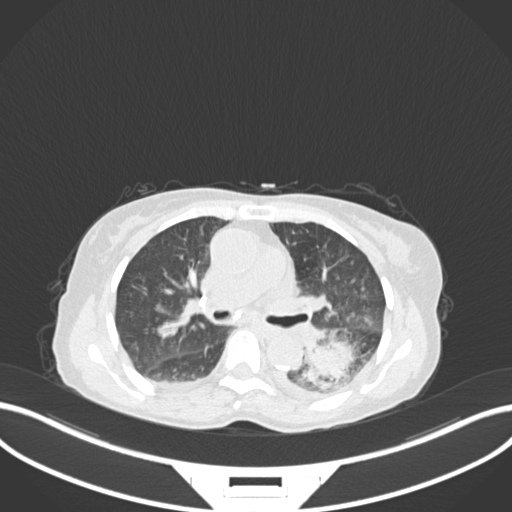
Chest CT, one axial slice; slice 103 of 233 in the series (ordered by position); reconstruction kernel B30f; lung window (W 1500 / L -600 HU); 1 mm slice thickness; 512 × 512 image matrix, field of view 400 × 400 mm. Patient: female, 78 years. From the clinical record (not read from this slice): clinical TNM (as recorded): T3 N0 M1.
Annotated regions visible in this slice (bounding box drawn by a radiologist):
- lung tumour (recorded histology: squamous cell carcinoma): box from (x=295, y=328) to (x=371, y=400) px